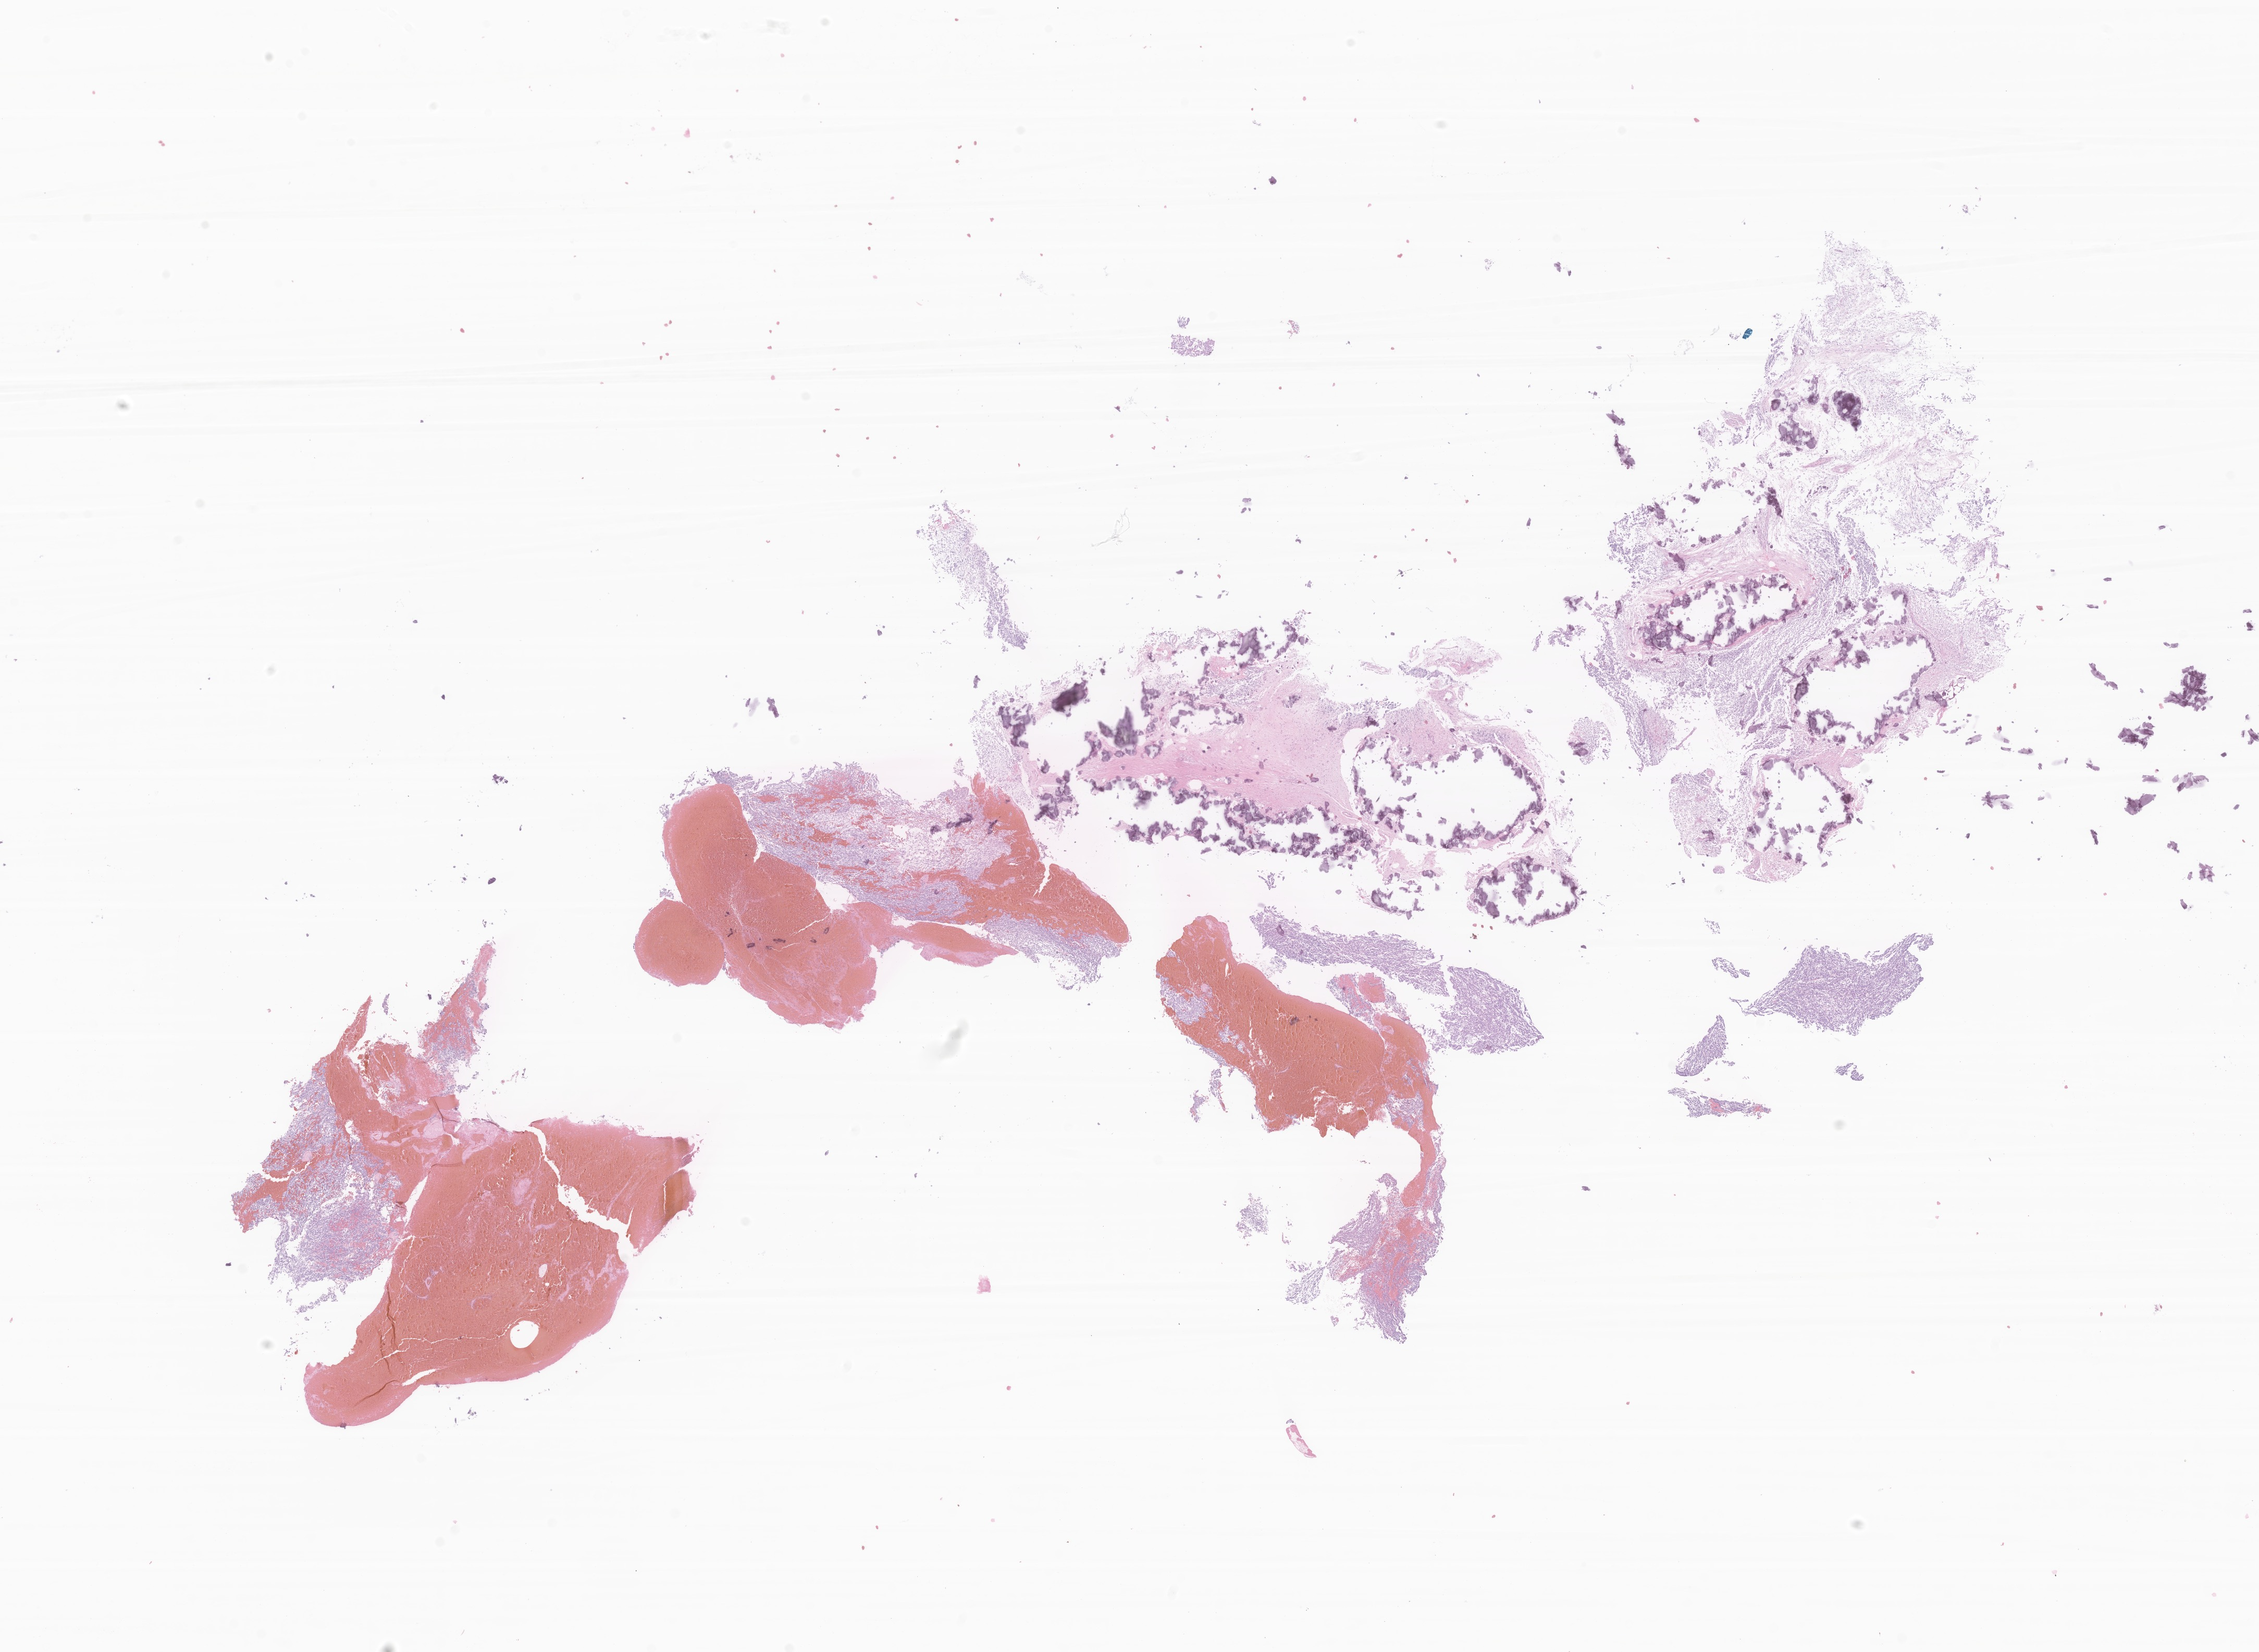
Hematoxylin and eosin (H&E) whole-slide image of tumor tissue from the pineal gland, low-resolution overview of the scanned area, about 18.3 x 13.4 mm, formalin-fixed, paraffin-embedded (FFPE) tissue. Female patient, age 226 months (18 years 10 months).
Recorded diagnosis: Pineoblastoma.